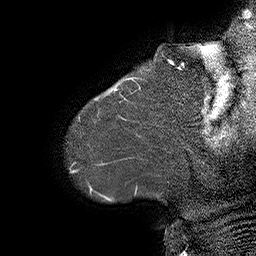
Breast MRI (dynamic contrast-enhanced), one sagittal slice. Slice 1 of 55 in the series (ordered by position). Dynamic contrast-enhanced series, time point 2 of 6 at this slice position (early post-contrast). 1.5 T. TE 4.5 ms, TR 32.4 ms. 3 mm slice thickness. 256 × 256 image matrix, field of view 180 × 180 mm. Female patient. Case-level facts recorded for this patient, not image findings: setting: breast cancer imaged before/during neoadjuvant chemotherapy; receptor status: HER2-positive.
Outlined on this slice (semi-automatically segmented with operator editing):
- analysis volume of interest (the breast-tissue region the enhancement analysis was run in; not a lesion): bounding box (x1, y1, x2, y2) in pixels: (80, 64, 163, 134)
- tumour enhancement mask (voxels above the 100 % enhancement threshold inside the analysis volume of interest): (95, 77, 140, 100)